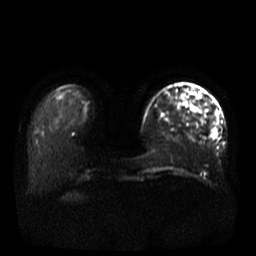
Breast MRI, one axial slice; position 9 of 37 along the scan axis; diffusion-weighted series; image 2 of 4 stored at this slice position (different b-values; order by instance number); 3 T; 5 mm slice thickness; 256 × 256 image matrix. Female patient.
Annotated regions visible in this slice (outlined manually by an expert reader):
- tumour on diffusion-weighted imaging: bounding box (x1, y1, x2, y2) in pixels: (210, 112, 217, 139)